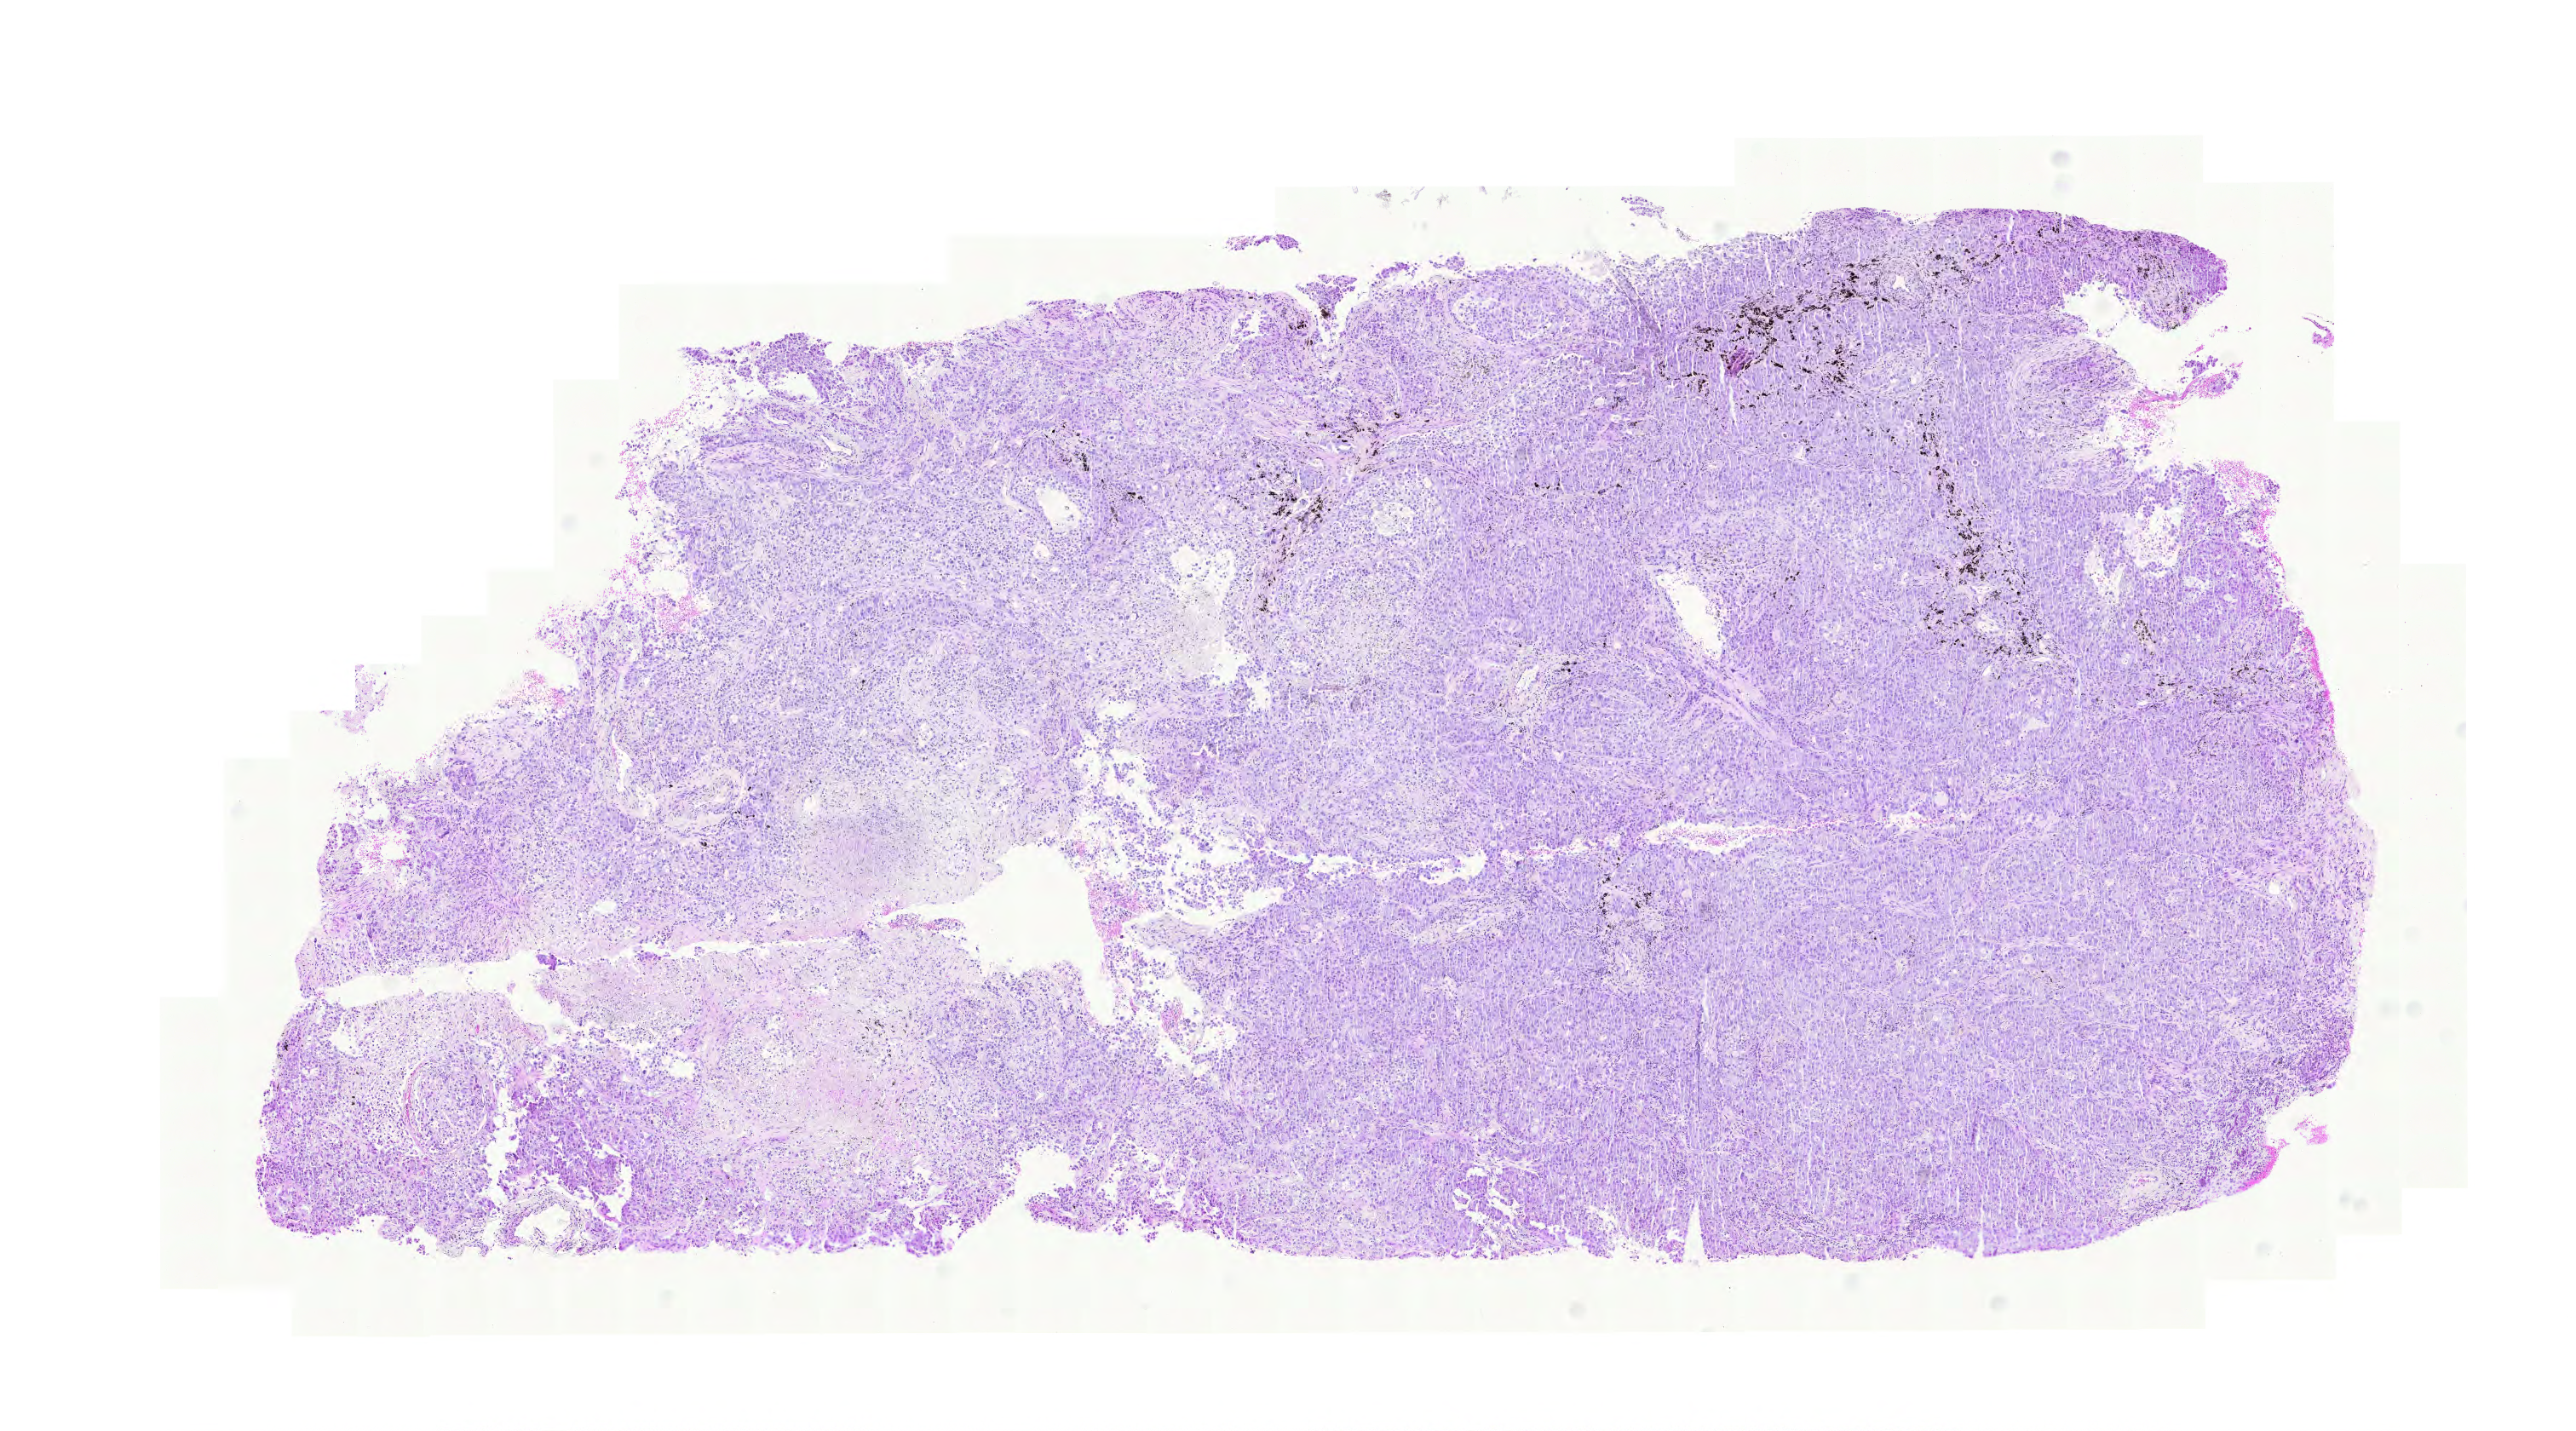
Hematoxylin and eosin (H&E) stained whole-slide image — a low-resolution overview of the entire scanned area, about 11.2 x 6.2 mm (acquisition: 20x scan), FFPE section, primary tumour sample from the lung. Male, age 76 years at initial diagnosis.
Diagnosis: Adenocarcinoma with mixed subtypes (upper lobe, lung). TNM: T4 N2 M0. AJCC pathologic stage: IIIB.